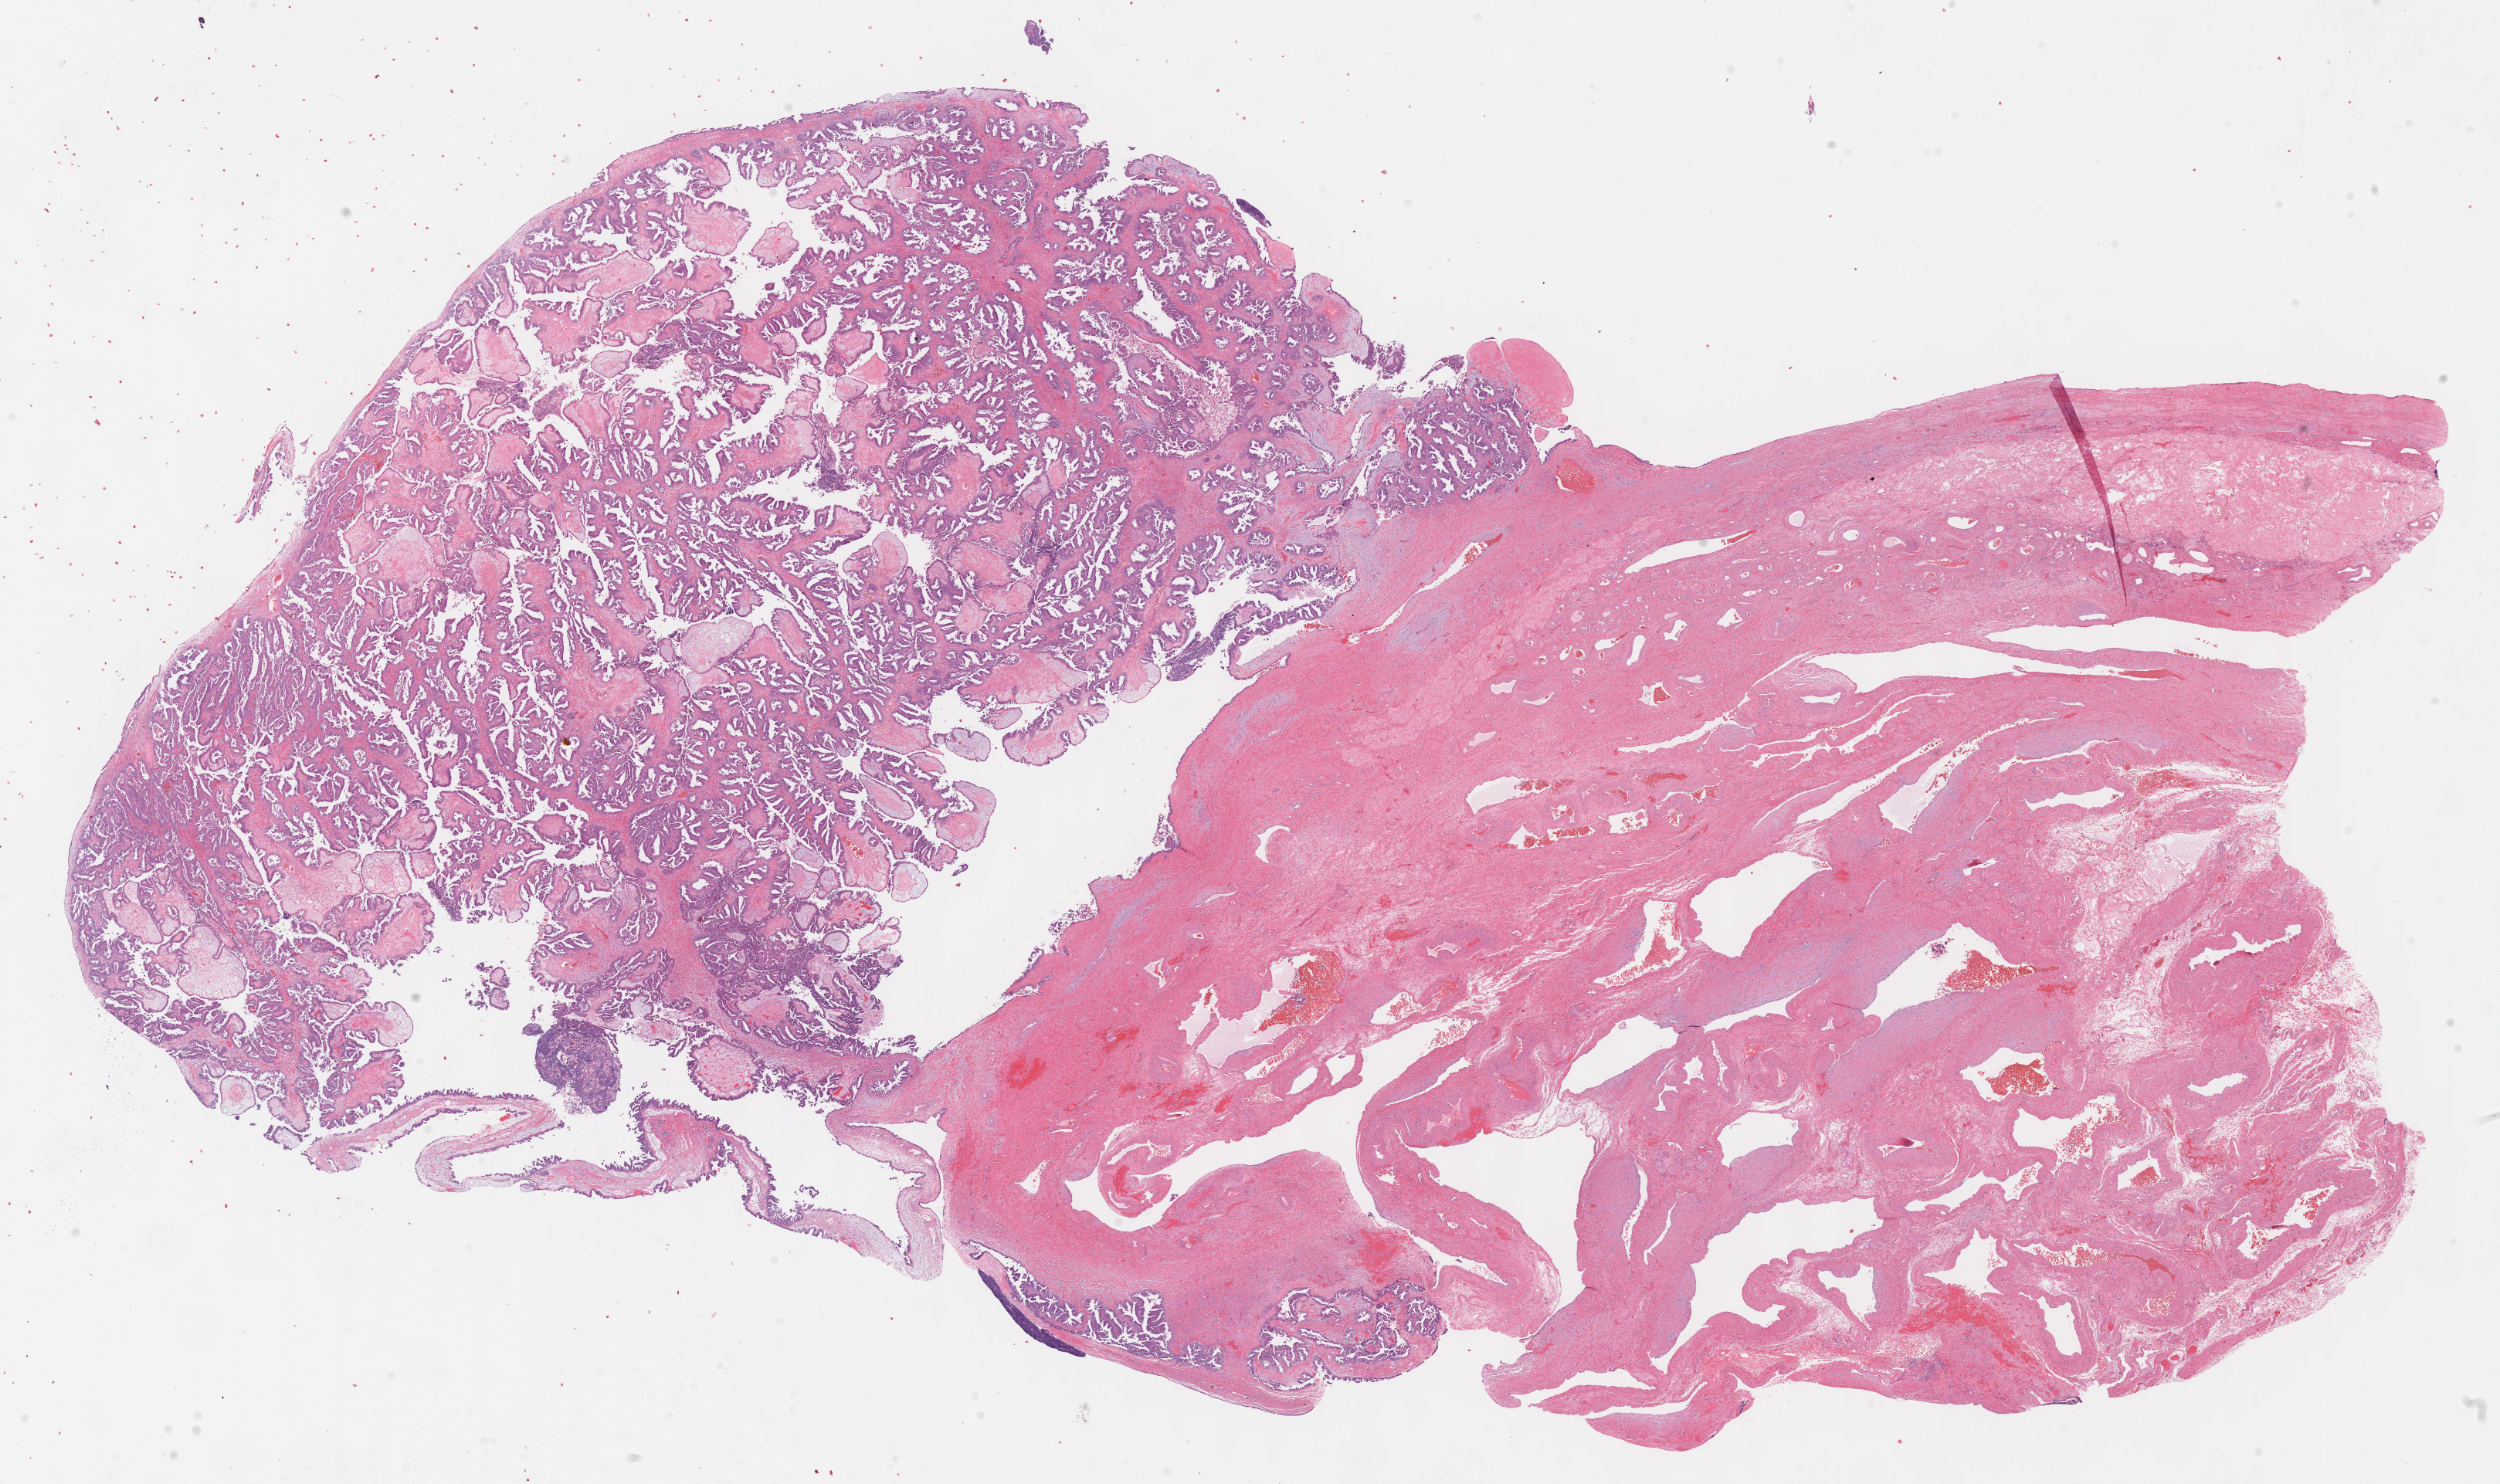
Digitized H&E-stained tissue section (whole slide) — shown as a low-resolution overview of the whole scanned area (about 26.2 x 15.5 mm, from a 40x scan); formalin-fixed paraffin-embedded (FFPE) diagnostic section; sample: primary tumour, ovary. Female patient; age at initial diagnosis 61 years. Histologic grade: GX (grade cannot be assessed).
Laterality: right. FIGO stage: IIC. Diagnosis: Papillary serous cystadenocarcinoma.